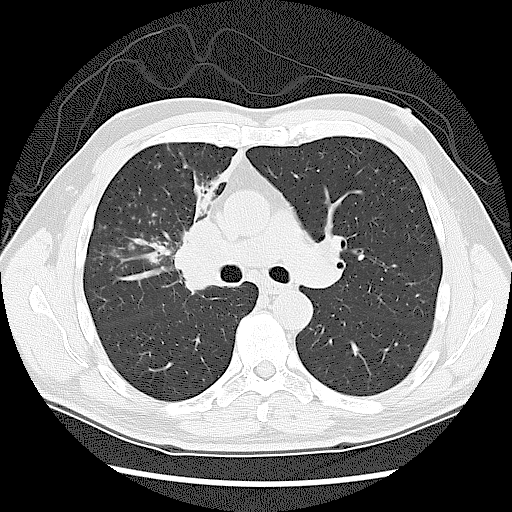
Chest CT (low-dose screening protocol), one axial image; first (baseline) screen; lung window (W 1500 / L -600 HU); slice 54 of 131 in the series. Male, age 60 years at enrolment.
- Lesion marked by an expert reader, bounding box <158,219,242,312> (left, top, right, bottom; pixels).
- No non-calcified nodule or mass ≥4 mm was recorded by the screening reader at this exam.
- Official screen result: negative screen, significant abnormalities not suspicious for lung cancer.
- Lung cancer was diagnosed 41 days after this screen: small cell carcinoma, NOS, right upper lobe, stage IIIA (AJCC 6th edition).